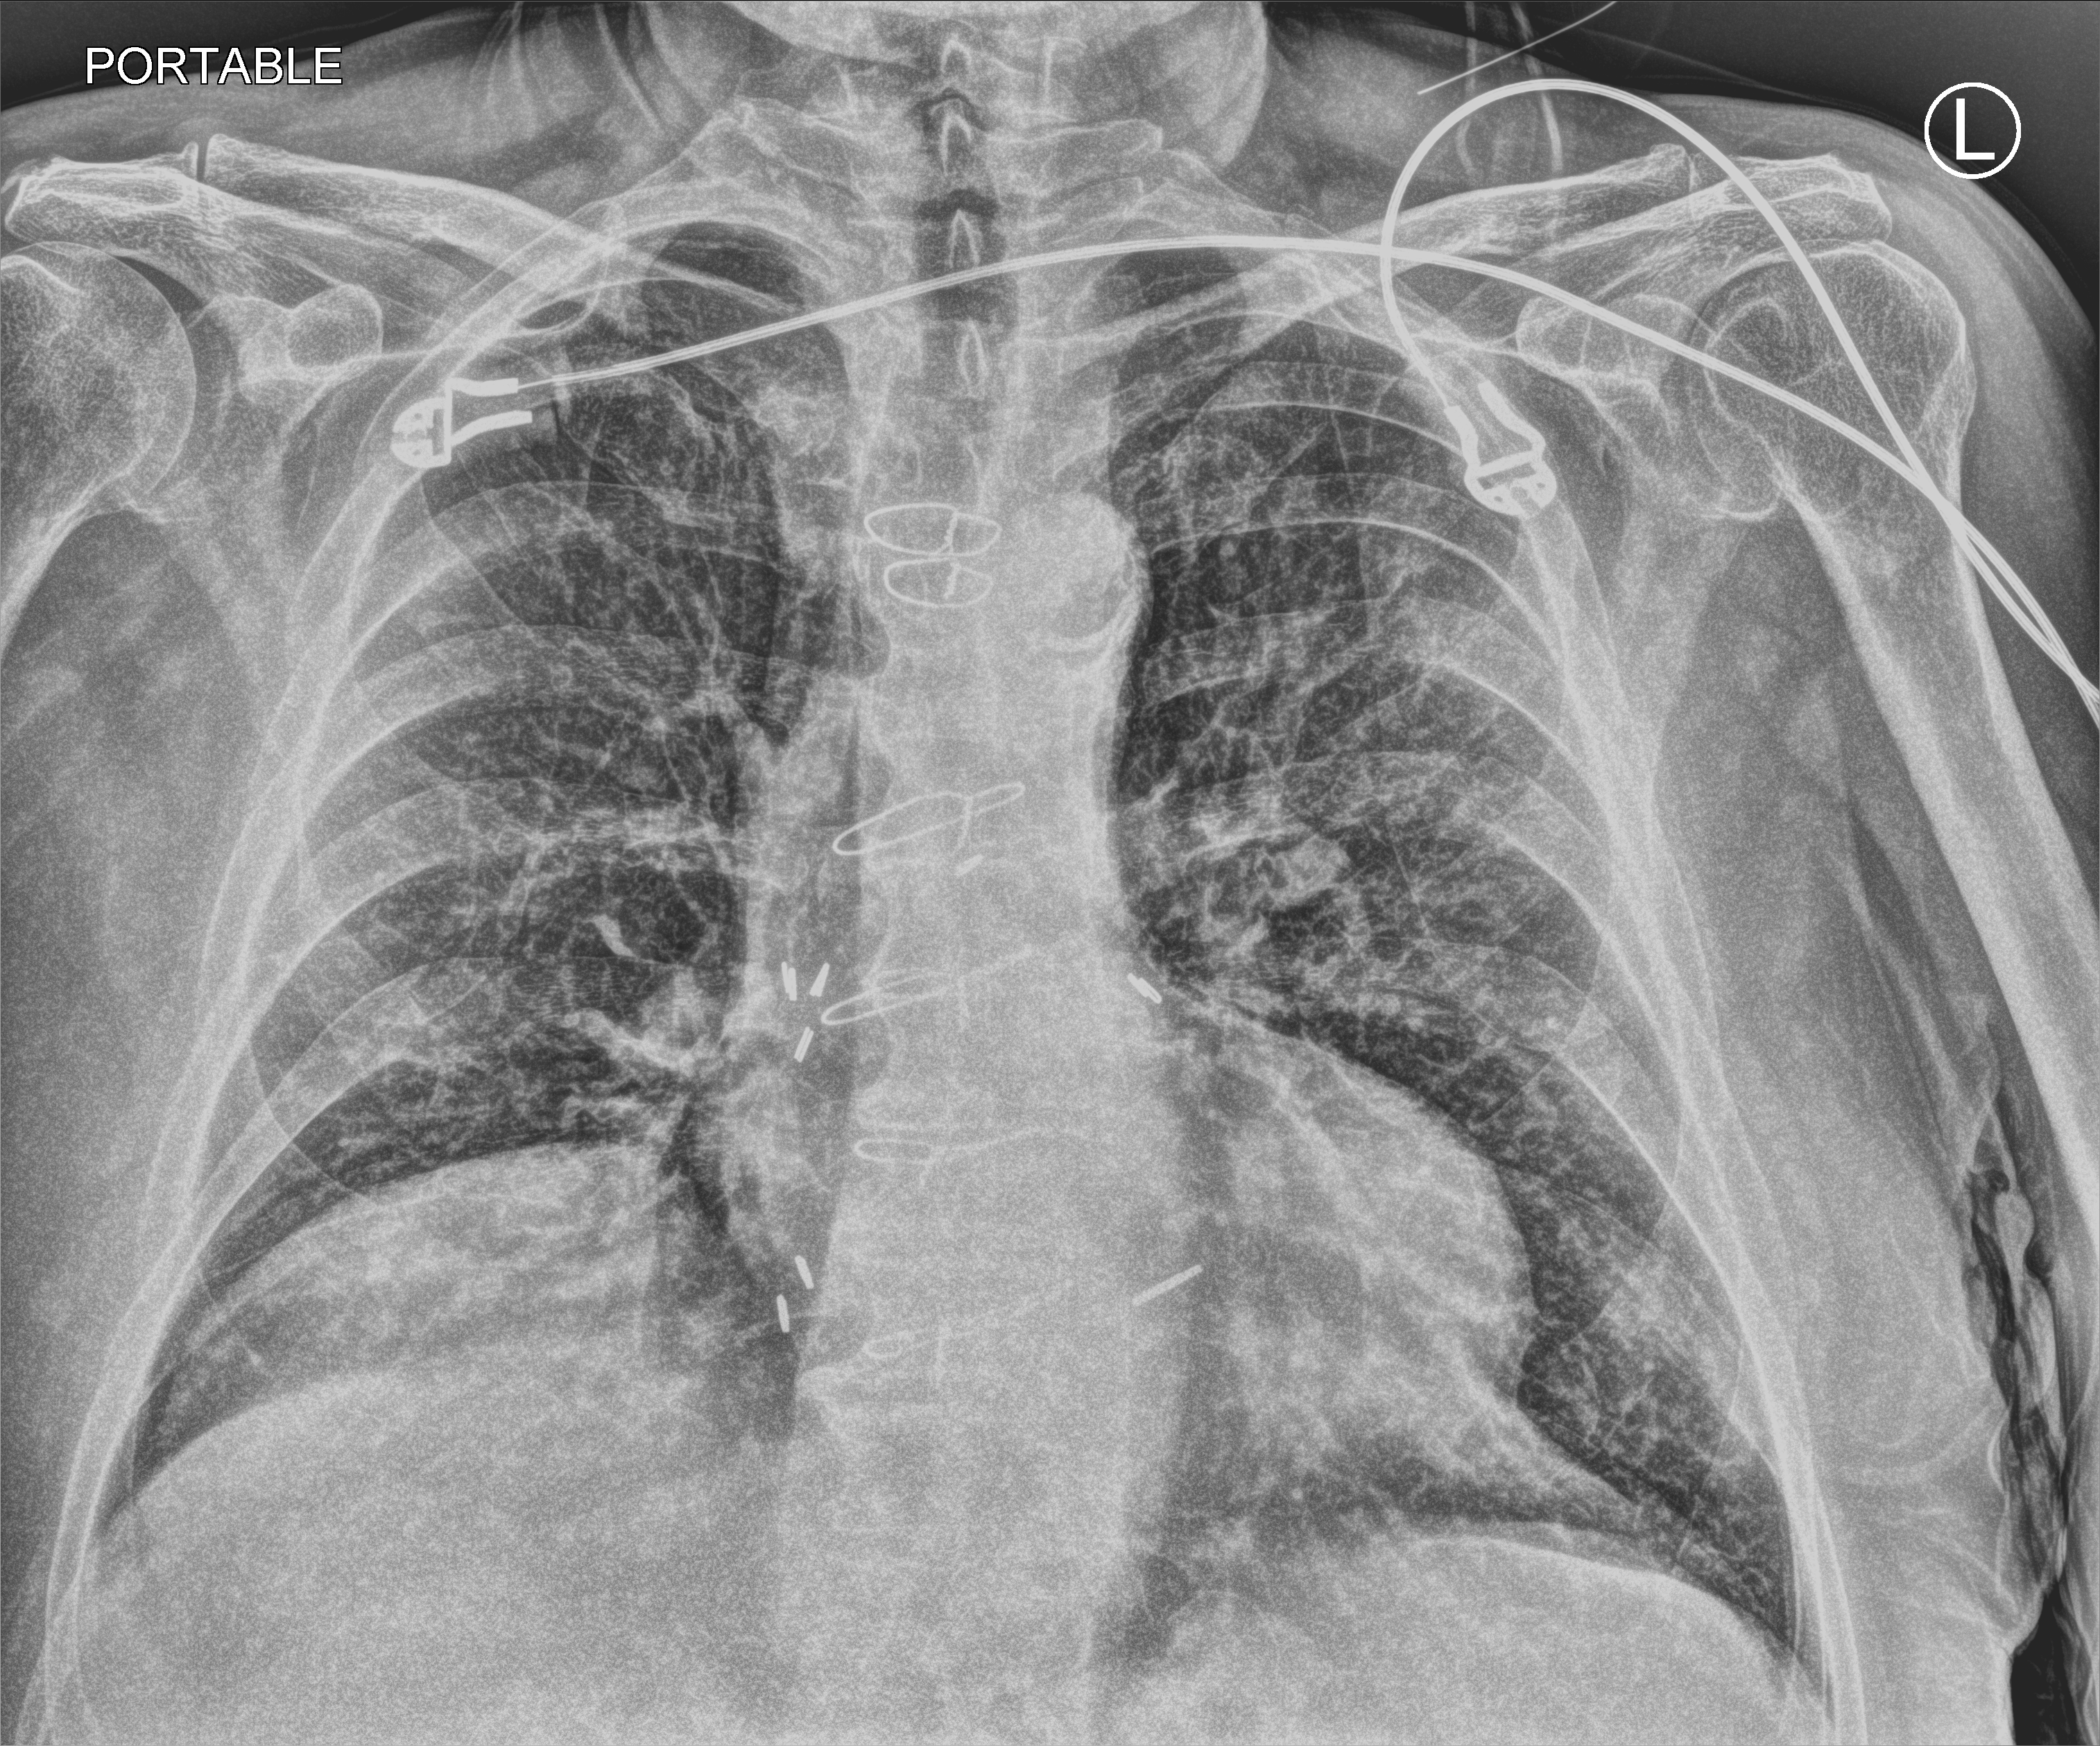
Portable chest radiograph, anteroposterior (AP) projection. Patient hospitalised with COVID-19; male, aged 75–90 years.
Admission-level facts for this patient (not findings on this image; timing relative to this image not recorded): admitted to intensive care during this hospital stay: no; mechanically ventilated during this hospital stay: no.